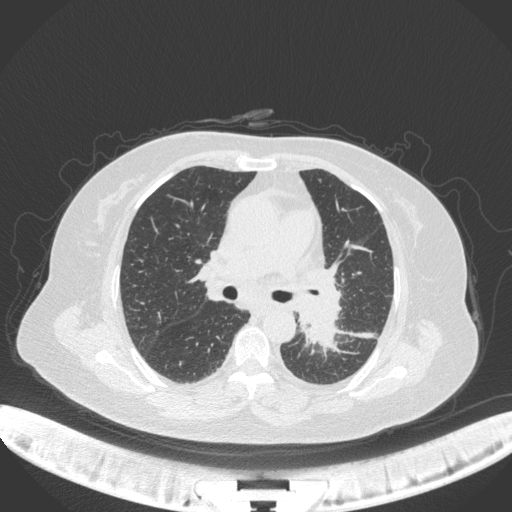
Chest CT, one axial slice. Position 206 of 328 along the scan axis. Reconstruction kernel B31f. 120 kVp. Lung window (W 1500 / L -600 HU). 1 mm slice thickness. 512 × 512 image matrix, field of view 400 × 400 mm. Patient: female, 69 years. Case-level facts recorded for this patient, not image findings: clinical TNM (as recorded): T2b N3 M1.
Structures marked on this image (bounding box drawn by a radiologist):
- lung tumour (recorded histology: adenocarcinoma): bounding box <294,306,345,352> (left, top, right, bottom; pixels)